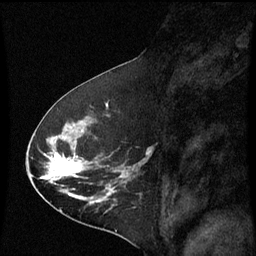
Breast MRI (dynamic contrast-enhanced), one sagittal slice; position 32 of 60 along the scan axis; dynamic contrast-enhanced series, image 2 of 3 at this slice position (ordered by acquisition); 1.5 T; TE 4.2 ms, TR 8.9 ms; 2 mm slice thickness; 256 × 256 image matrix, field of view 200 × 200 mm. Female patient, age 53 years. Case-level facts recorded for this patient, not image findings: setting: breast cancer imaged before/during neoadjuvant chemotherapy; receptor status: HR-positive, HER2-negative.
Outlined on this slice (semi-automatically segmented with operator editing):
- analysis volume of interest (the breast-tissue region the enhancement analysis was run in; not a lesion): box from (x=32, y=100) to (x=145, y=221) px
- tumour enhancement mask (voxels above the 70 % enhancement threshold inside the analysis volume of interest): (x=42, y=156)–(x=117, y=203)